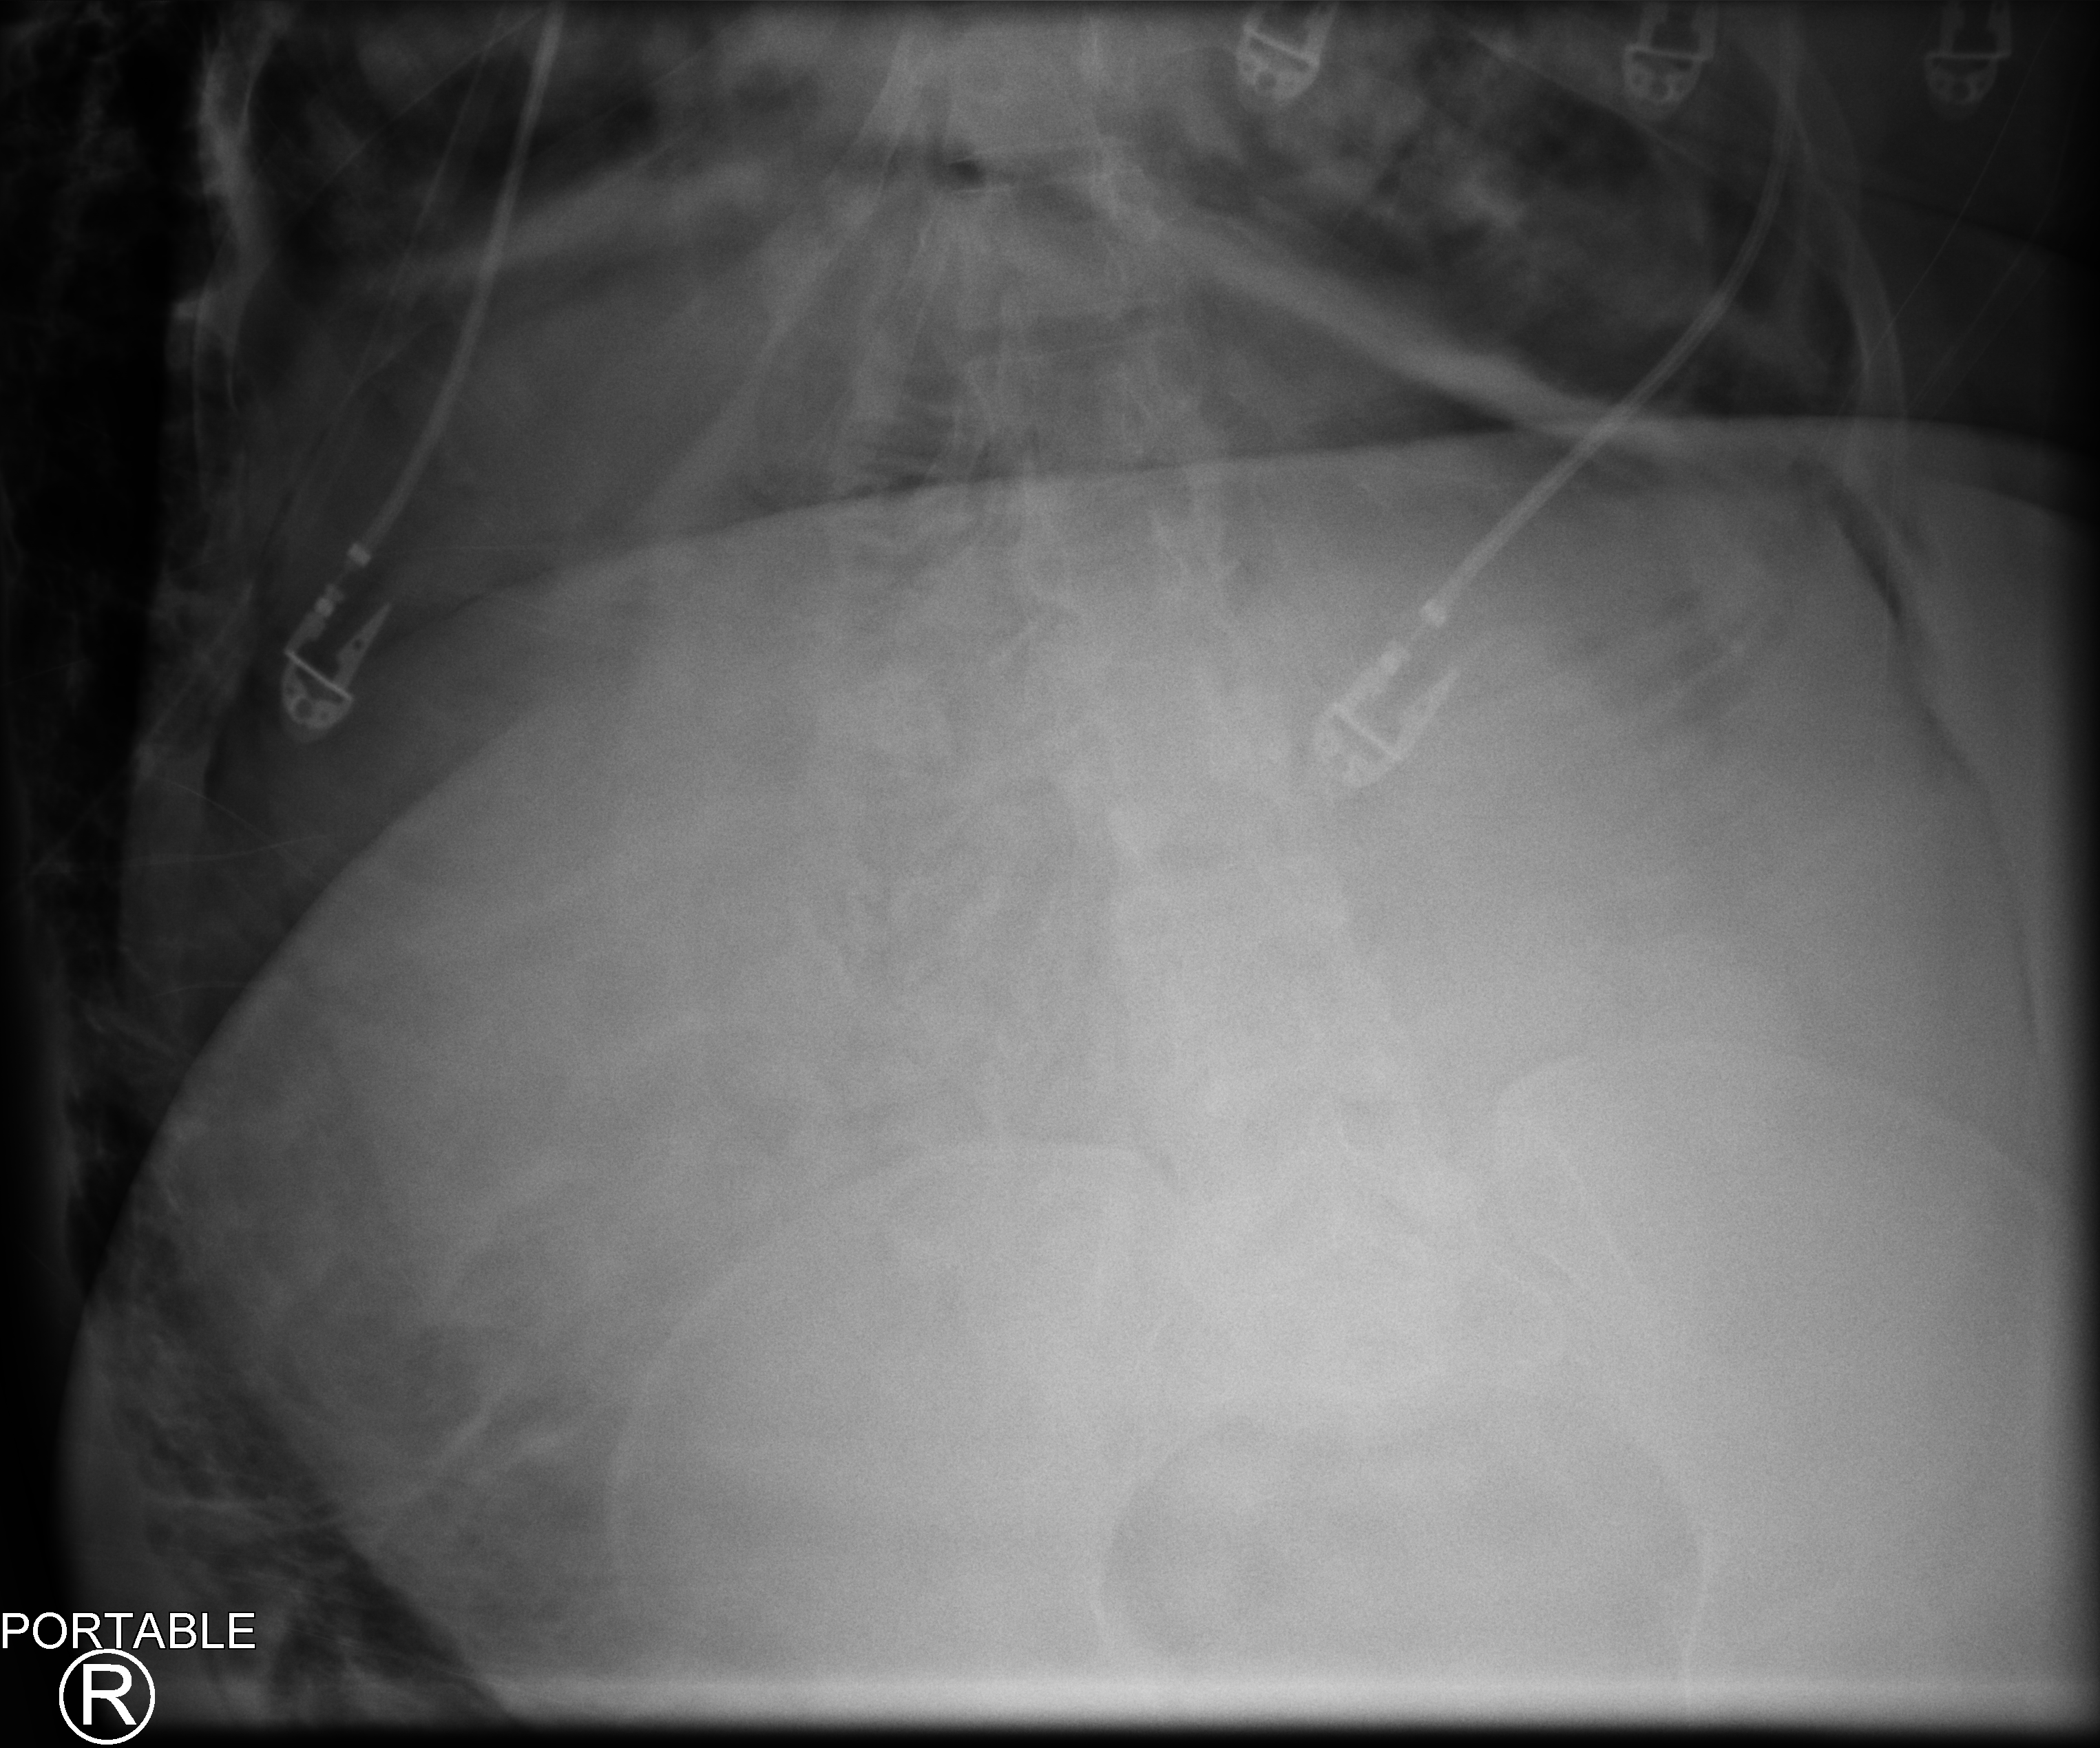
Portable abdomen radiograph, anteroposterior (AP) projection. Patient hospitalised with COVID-19, aged 18–59 years.
Admission-level facts for this patient (not findings on this image; timing relative to this image not recorded): mechanically ventilated during this hospital stay: yes; COPD (admission record): no.